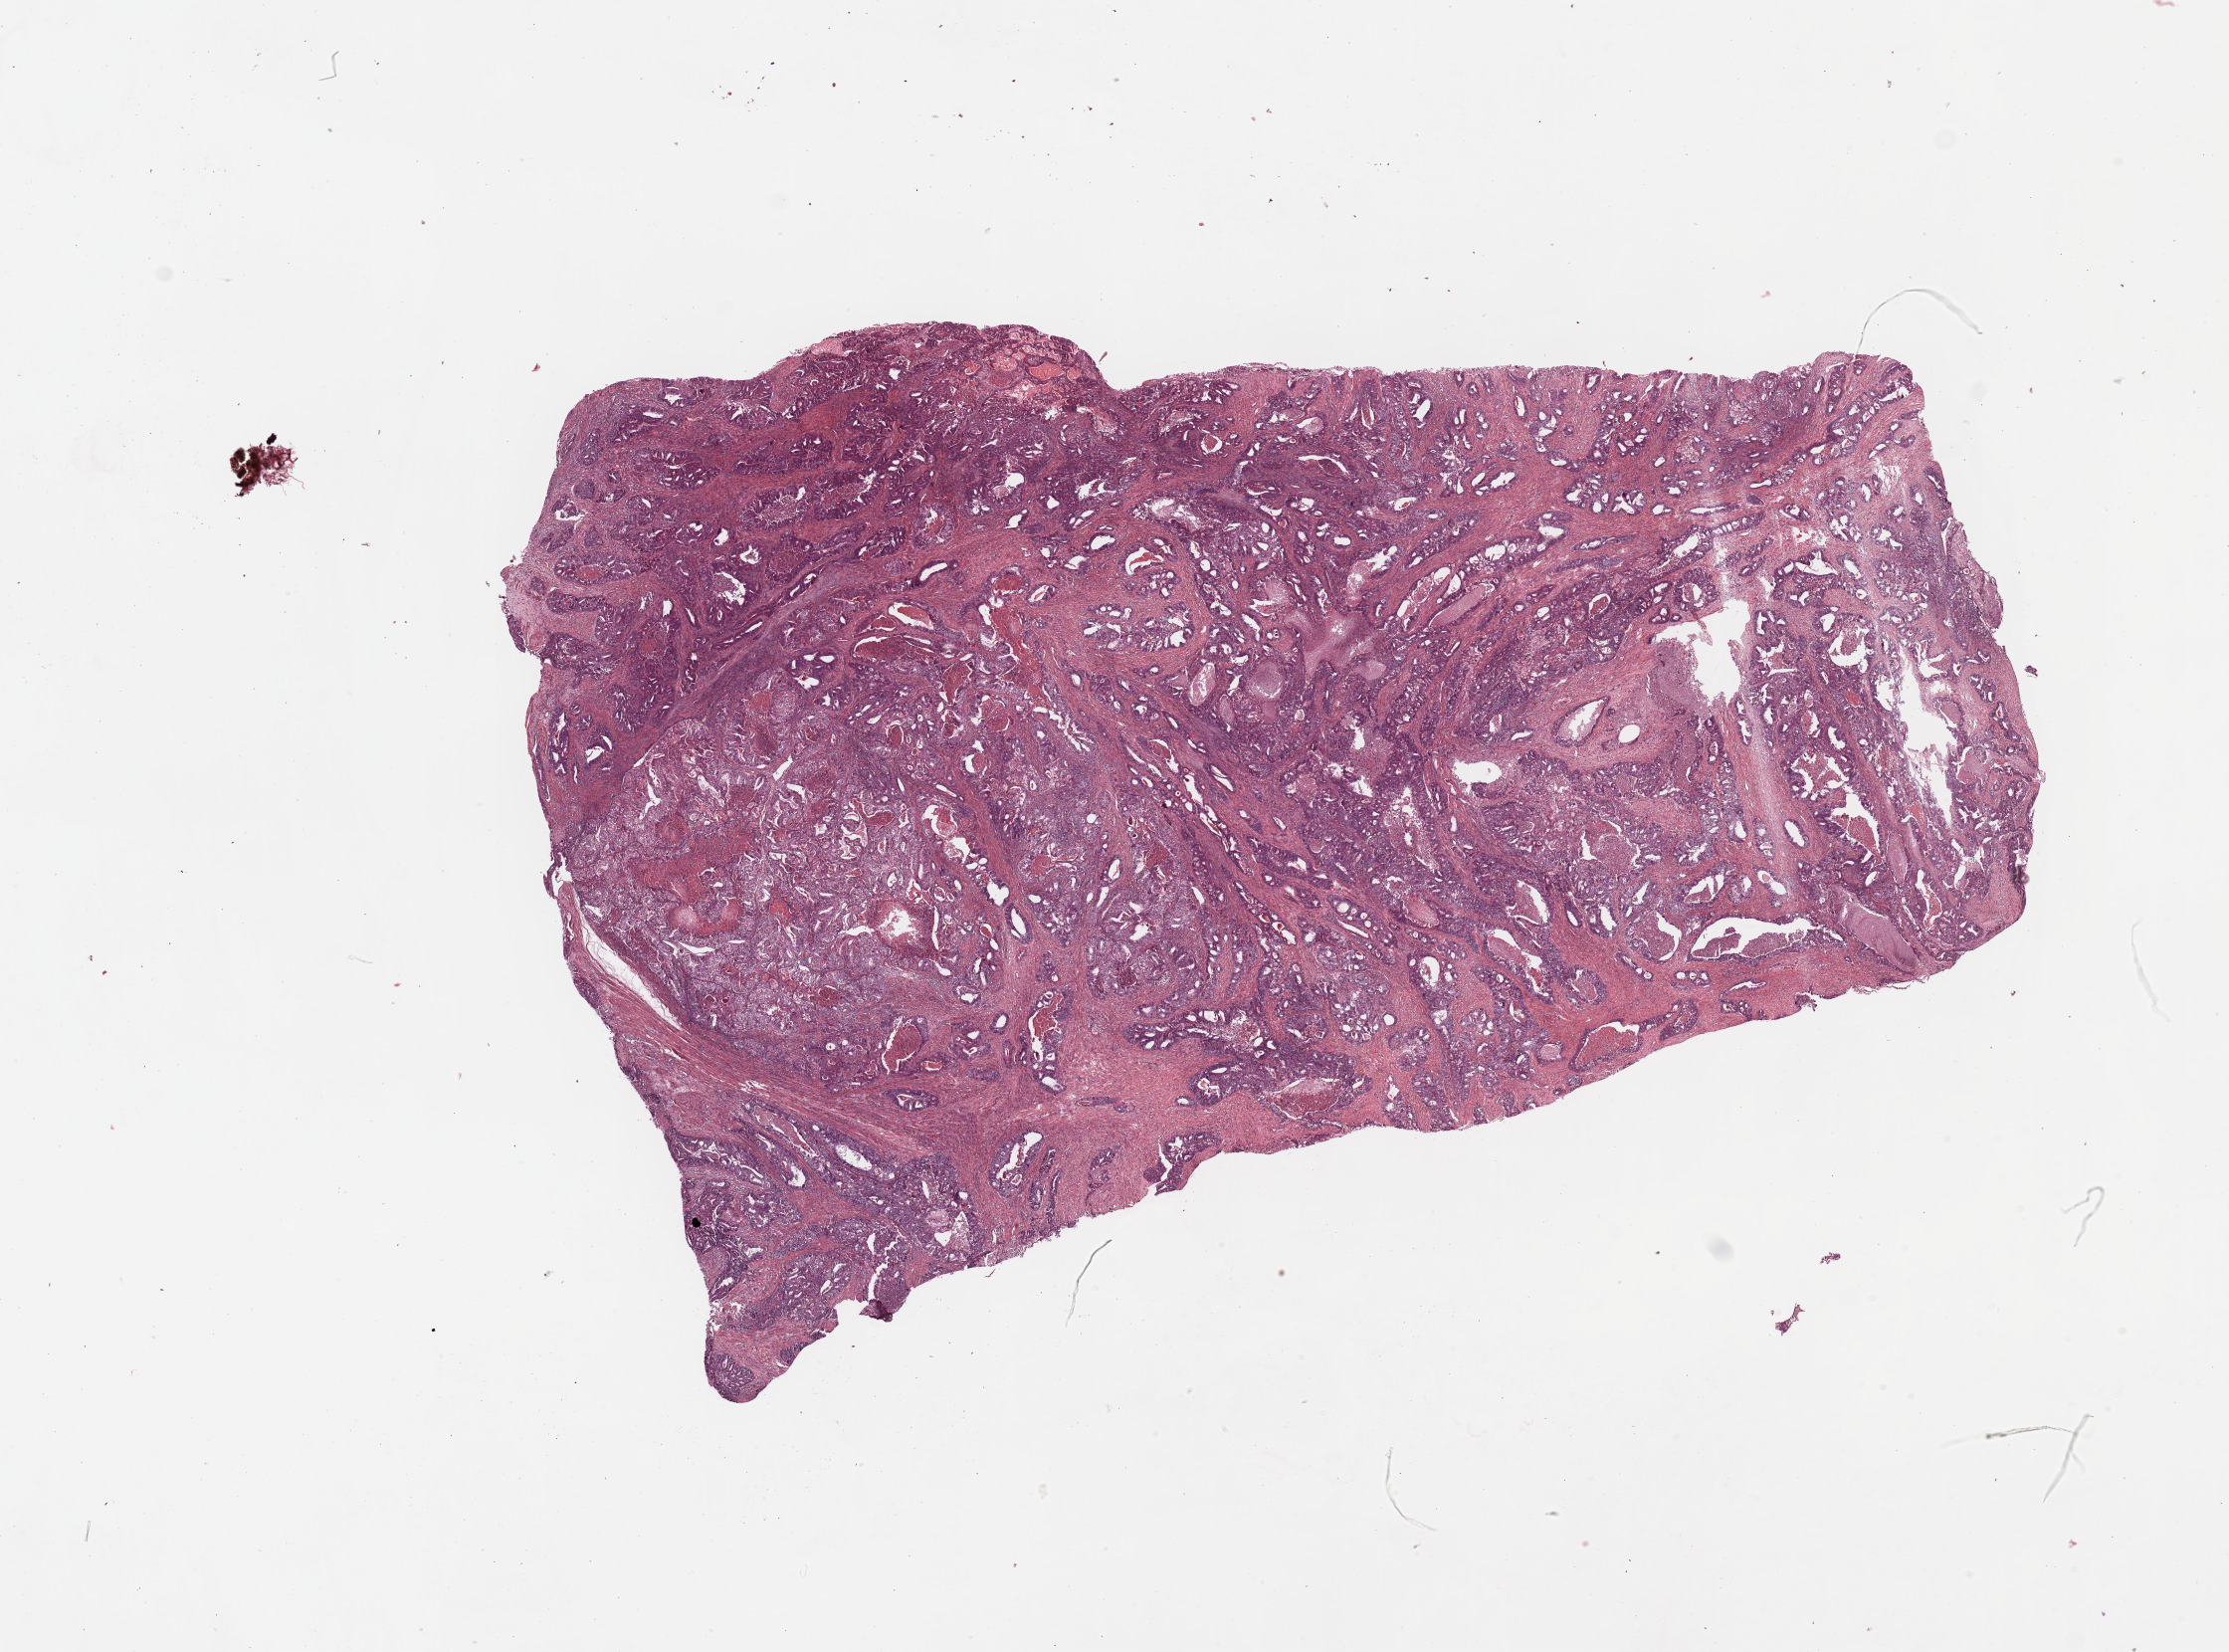
H&E whole-slide image, shown as a low-resolution overview of the whole scanned area (about 17.7 x 13.1 mm, from a 20x scan). Tumour tissue sample, sampled site: uterus. Female, 68 y/o. Histologic grade: G2 (moderately differentiated). Slide review estimates, as recorded: tumour nuclei 90%, necrosis 3%.
AJCC pathologic stage: I. Diagnosis: Endometrioid adenocarcinoma, NOS.